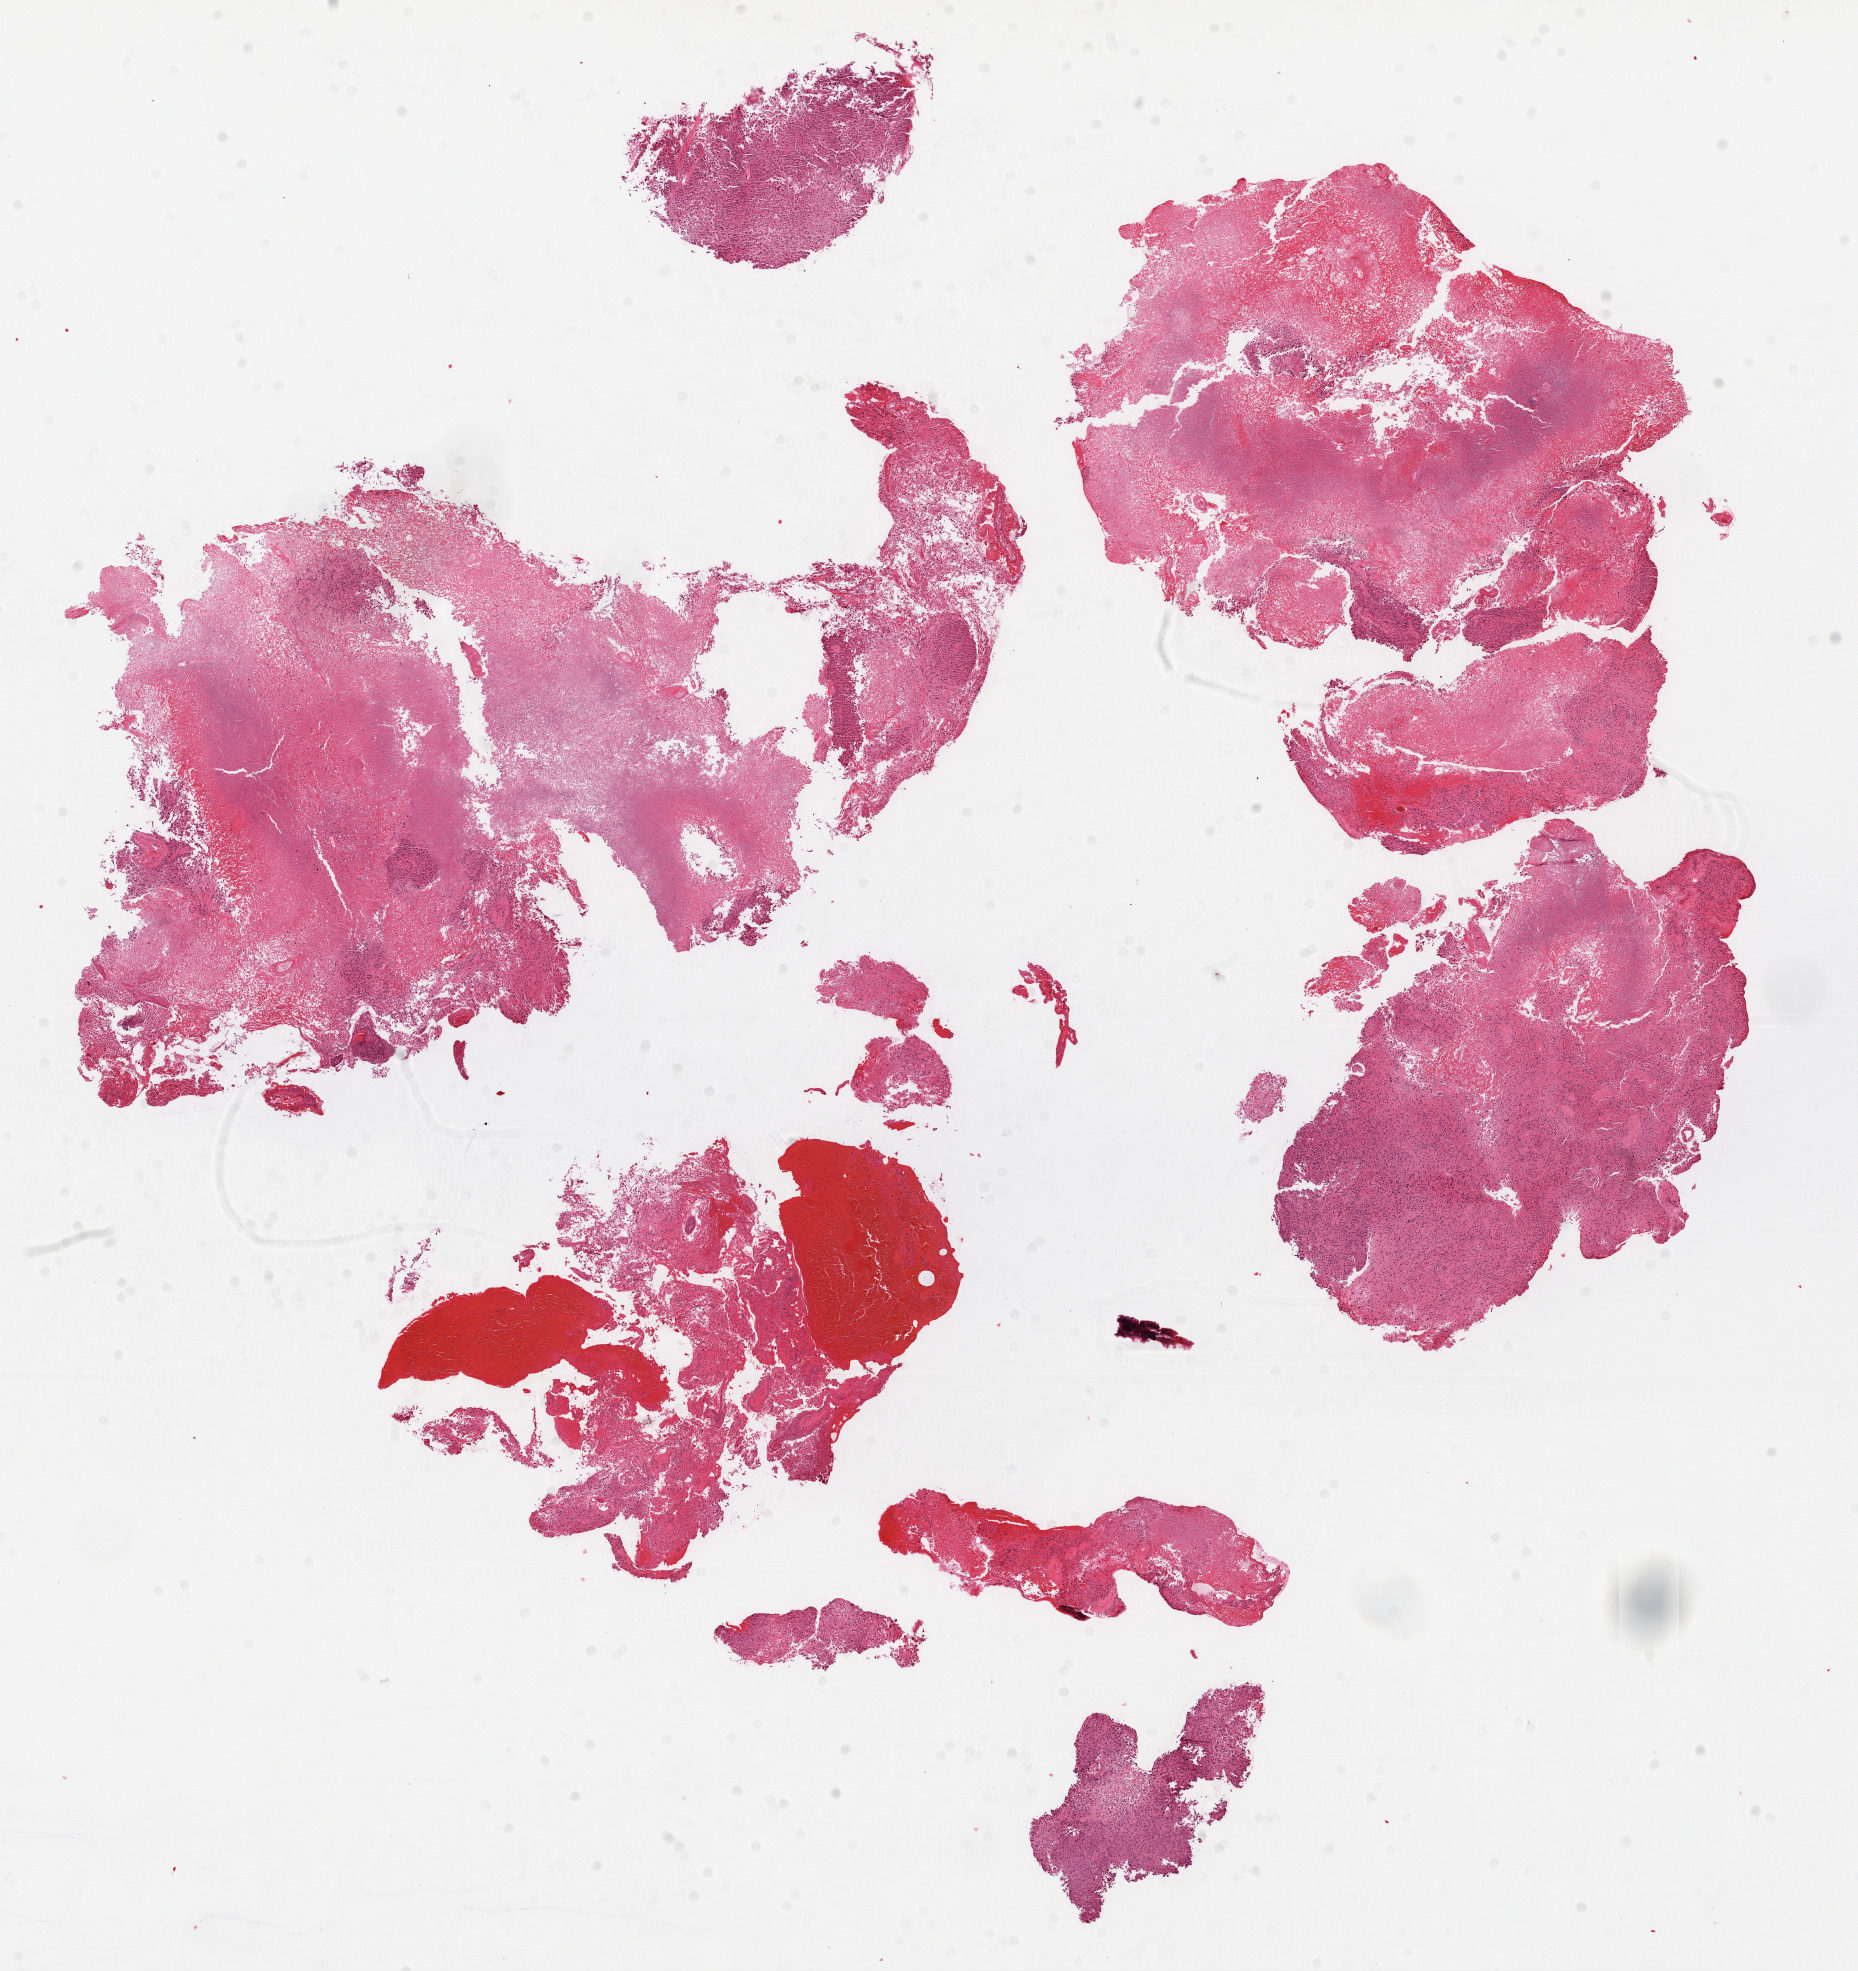
H&E-stained whole-slide image — low-resolution overview of the scanned area, about 15.0 x 15.9 mm, formalin-fixed paraffin-embedded (FFPE) diagnostic section, brain, primary tumour sample. Male, age 78 years at initial diagnosis.
* pathologic diagnosis: Glioblastoma